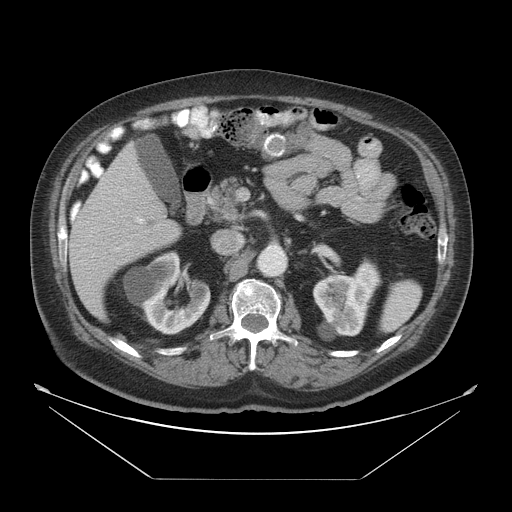
Contrast-enhanced abdominal CT, one axial slice. Position 24 of 45 along the scan axis. Reconstruction kernel STANDARD. Intravenous contrast given. Soft-tissue window (W 400 / L 40 HU). 512 × 512 image matrix. Male patient, age 87 years. From the clinical record (not read from this slice): diagnosis: colorectal cancer liver metastases, imaged before liver resection; multiple liver metastases: no; largest metastasis: 4.5 cm; chemotherapy before resection: no.
Outlined on this slice (outlined manually by an expert reader):
- liver: bounding box (x1, y1, x2, y2) in pixels: (69, 142, 182, 322)
- portal vein (with intrahepatic branches): (123, 189, 144, 223)